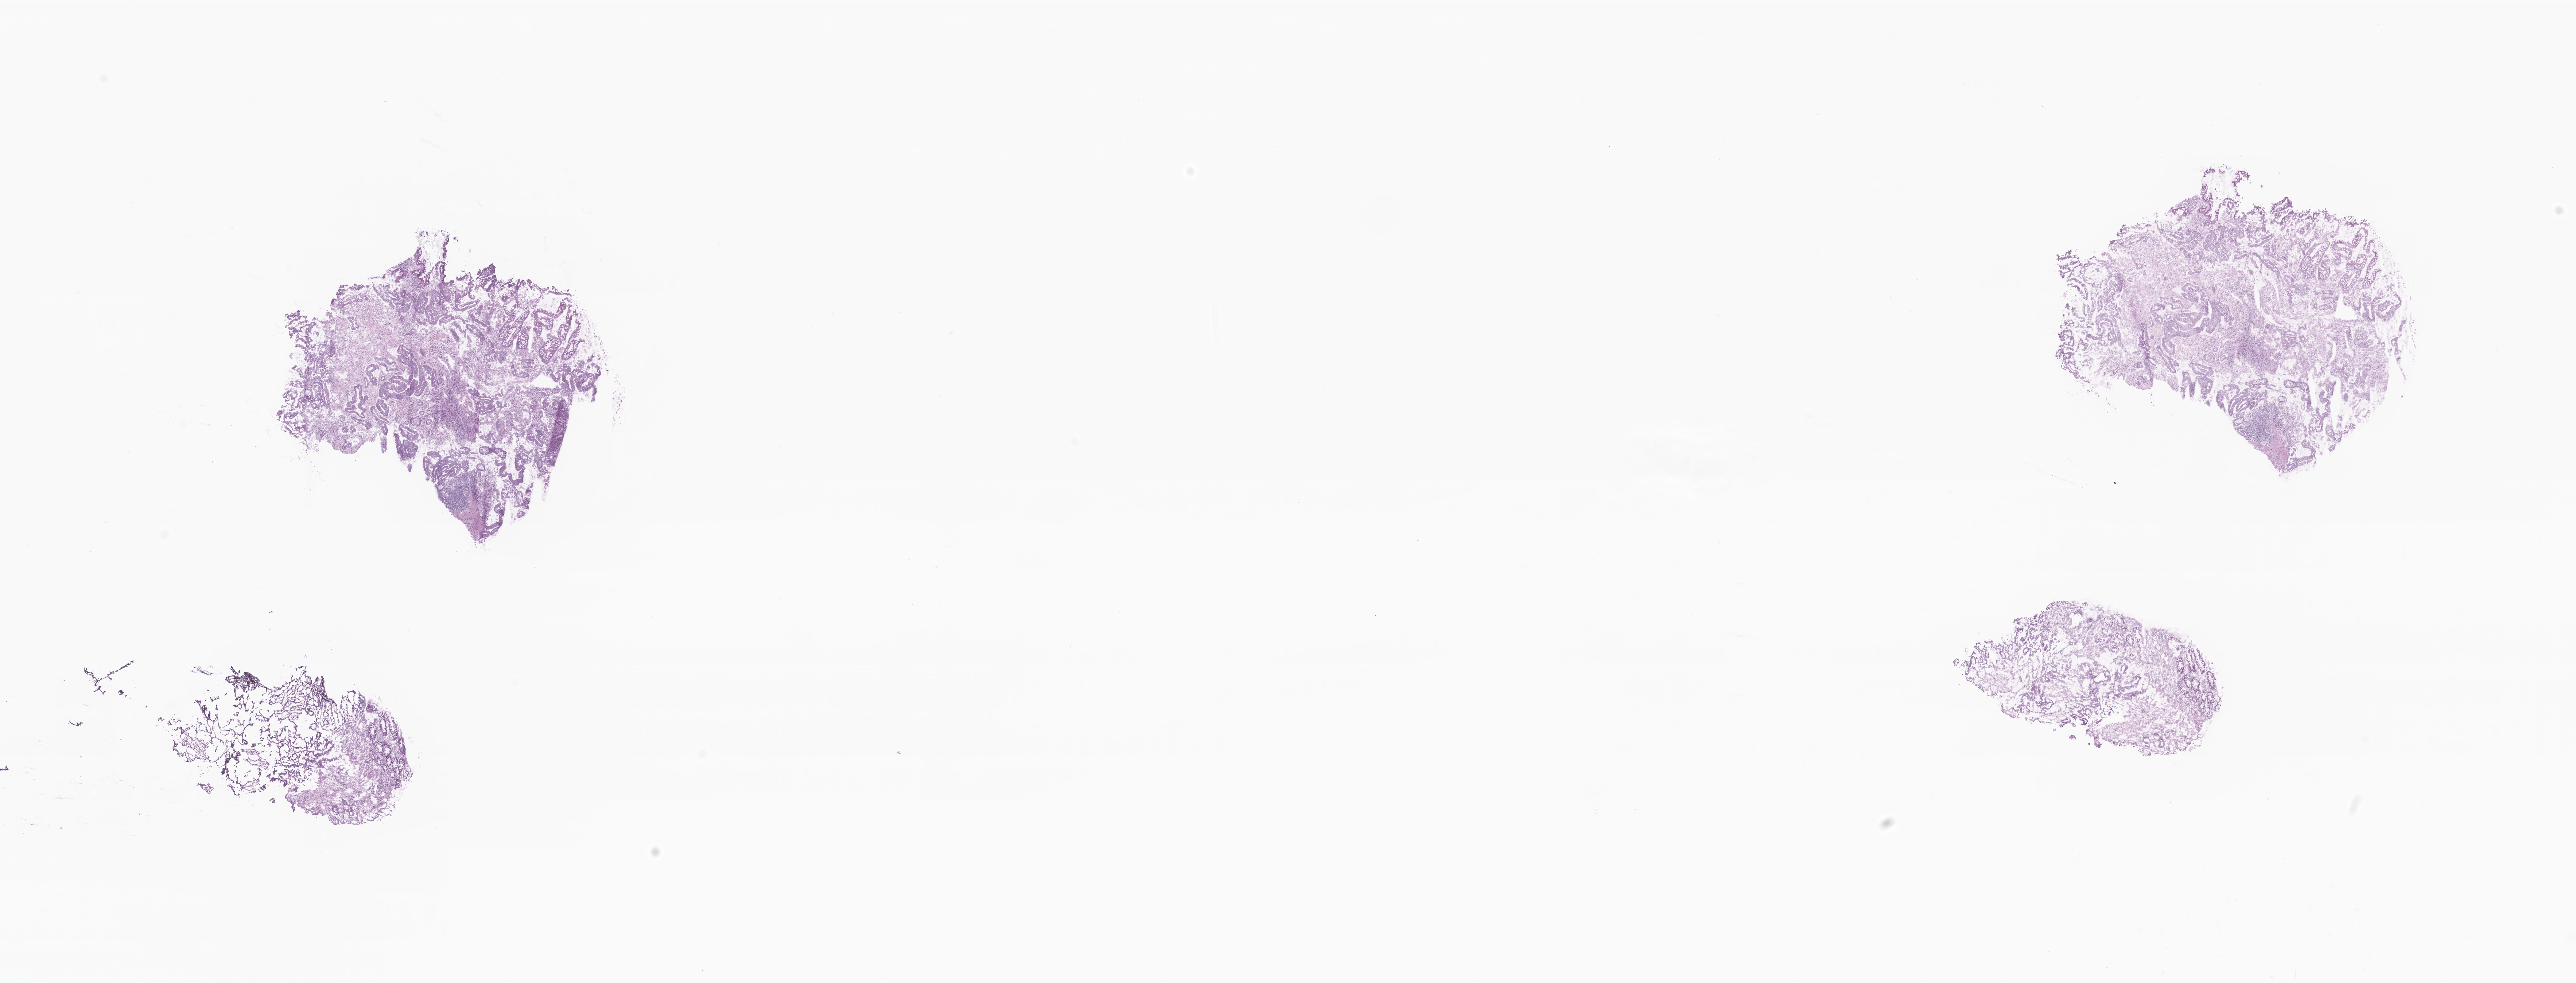
Digitized haematoxylin and eosin-stained section — whole scanned area (about 29.8 x 11.4 mm) shown as a low-resolution overview; cryosection; primary tumor; anatomic site: hepatic flexure of colon. Male, age 70 years at initial diagnosis. Slide review estimates, as recorded: tumor cells 35%, tumor nuclei 40%, stromal cells 50%, necrosis 0%, normal cells 15%. Inflammatory infiltration, as recorded: lymphocyte infiltration 100%, monocyte infiltration 0%, neutrophil infiltration 0%.
- histologic diagnosis: Adenocarcinoma, NOS